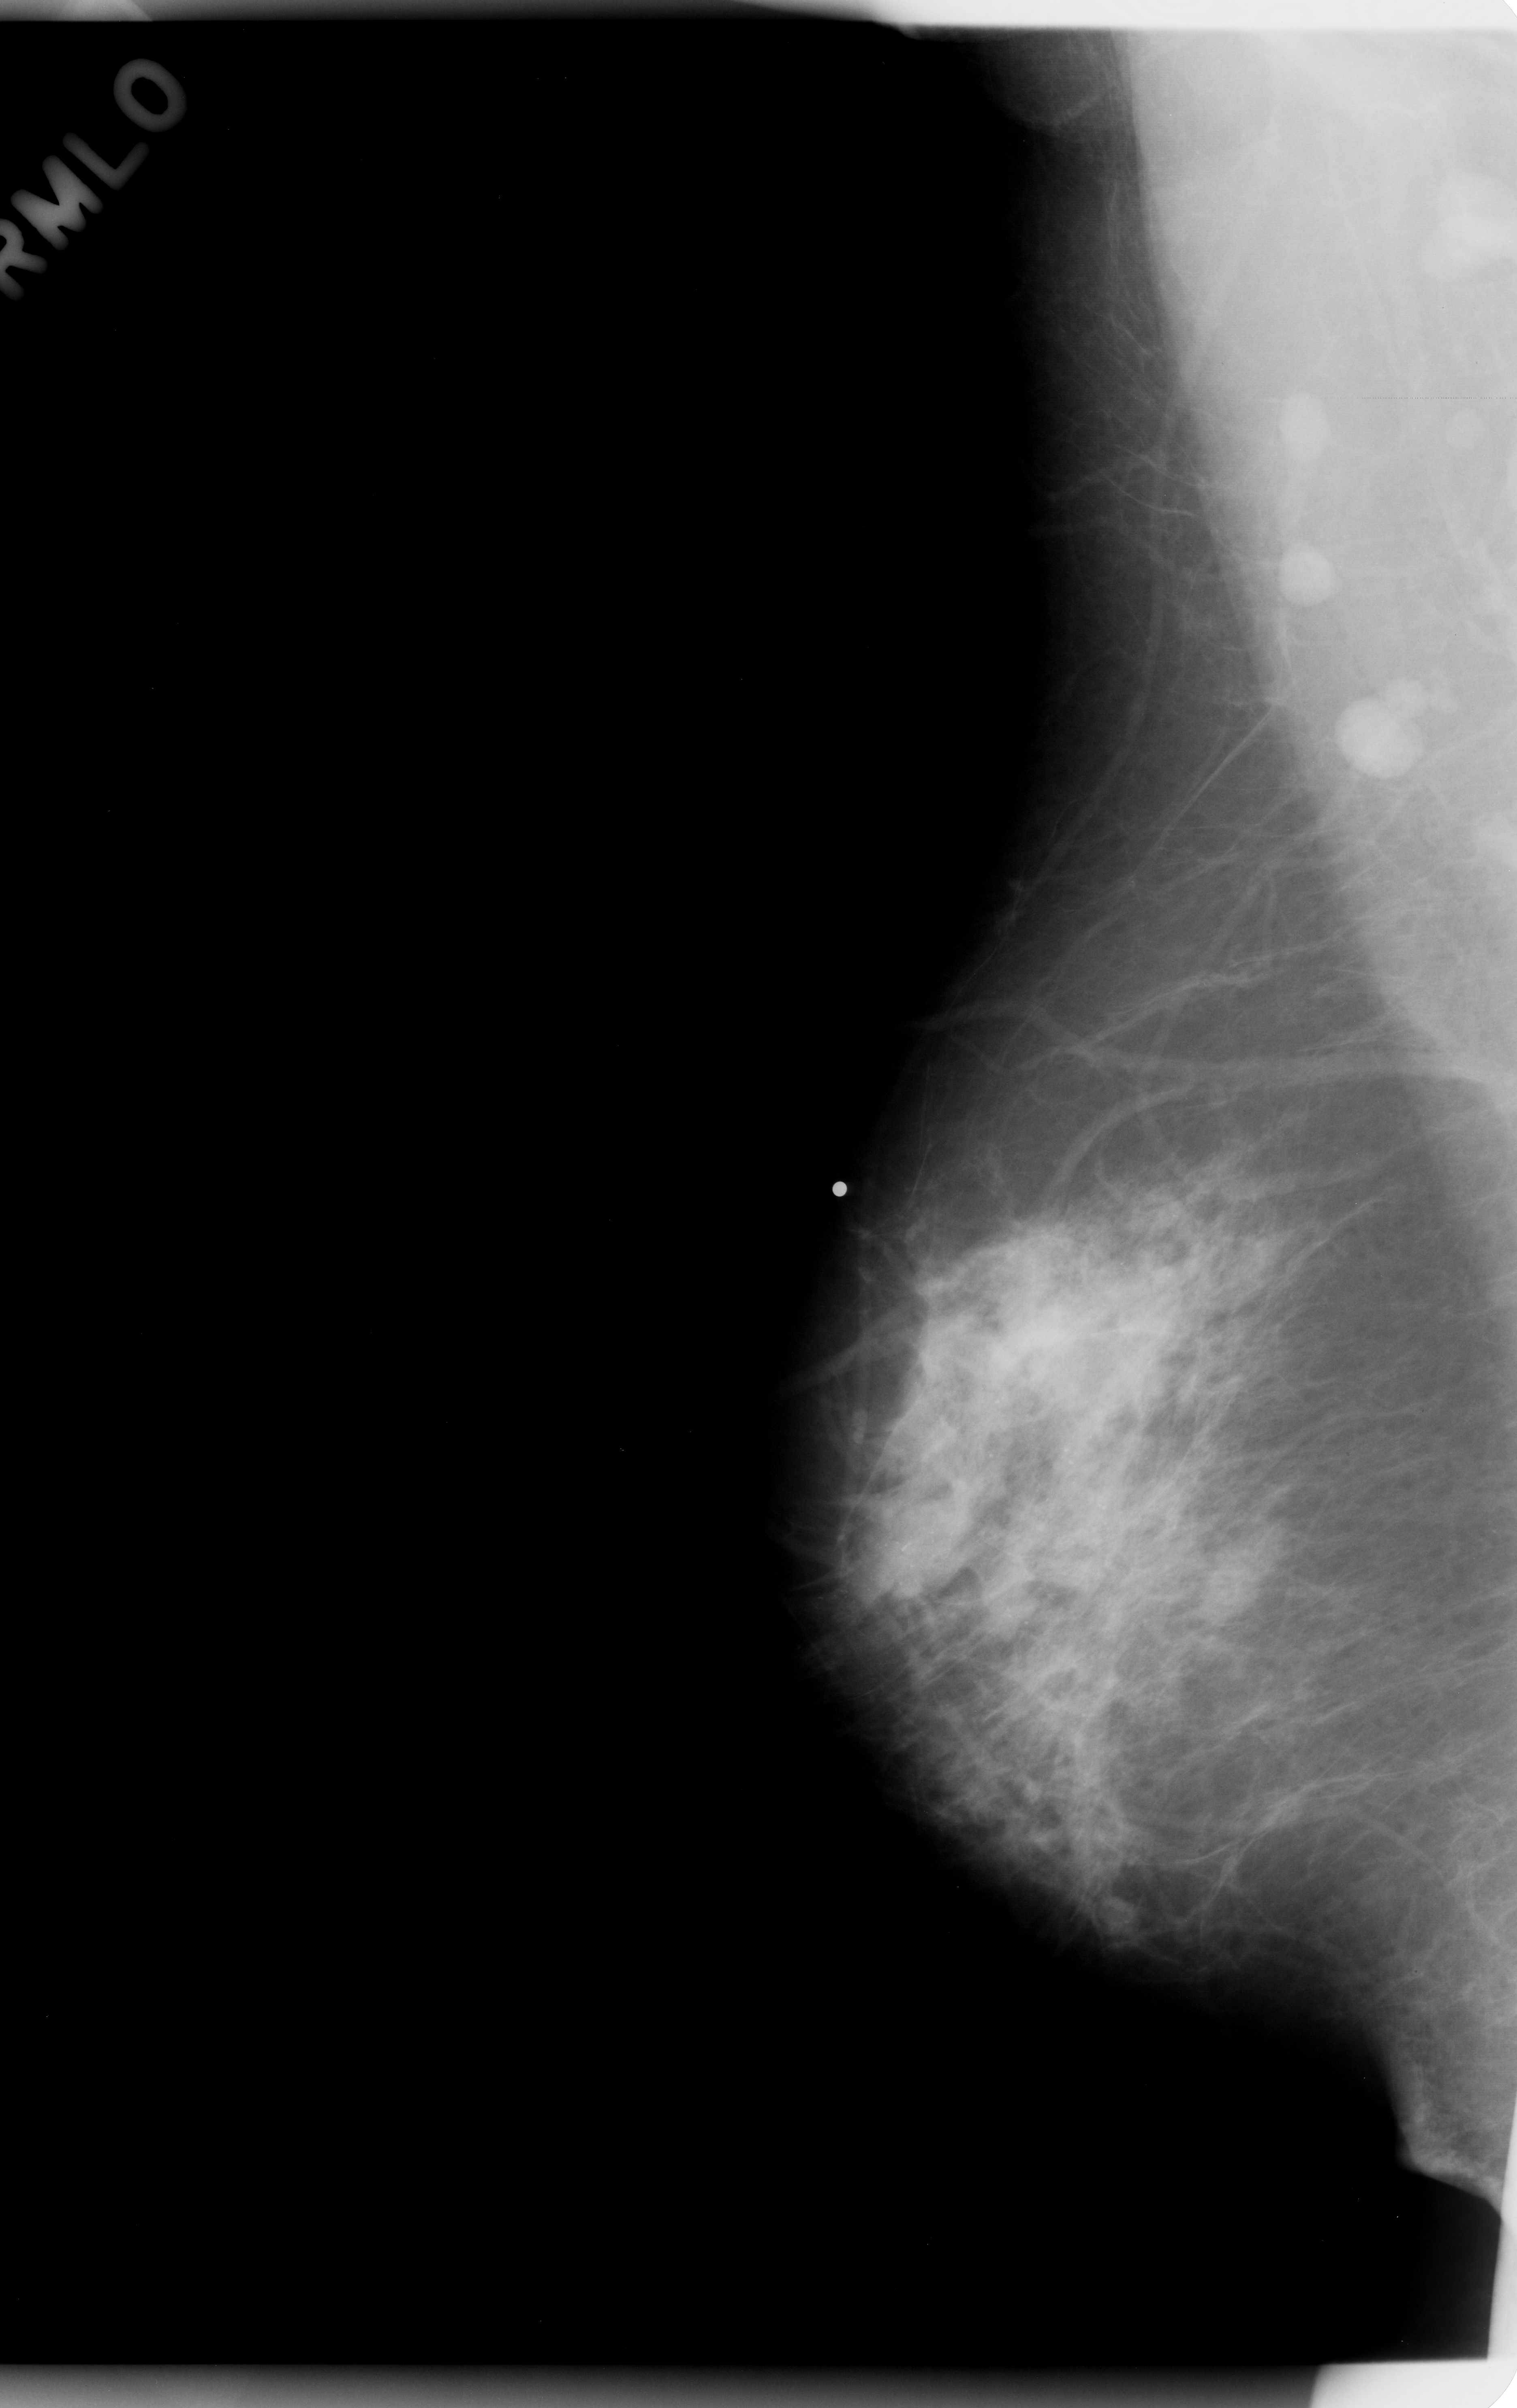
Digitized screen-film mammogram, right breast, MLO view, BI-RADS breast density category 2 (scale 1–4).
- Finding: calcifications, morphology pleomorphic, distribution regional; BI-RADS assessment category 5; pathology (as recorded): malignant.